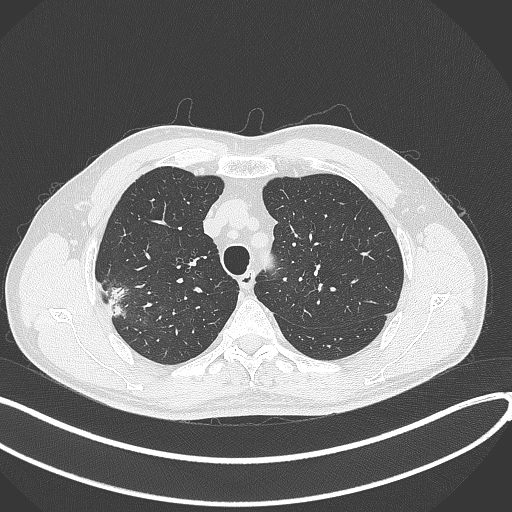
Chest CT, one axial slice. Slice 329 of 381 in the series (ordered by position). 120 kVp. Lung window (W 1500 / L -600 HU). 1 mm slice thickness. 512 × 512 image matrix, field of view 400 × 400 mm. Male patient, age 62 years. Case-level facts recorded for this patient, not image findings: clinical TNM (as recorded): T1c N0 M0; histopathological grade: G2-3.
Outlined on this slice (rectangle marked by the reading radiologist):
- lung tumour (recorded histology: adenocarcinoma): bounding box (x1, y1, x2, y2) in pixels: (104, 284, 128, 320)